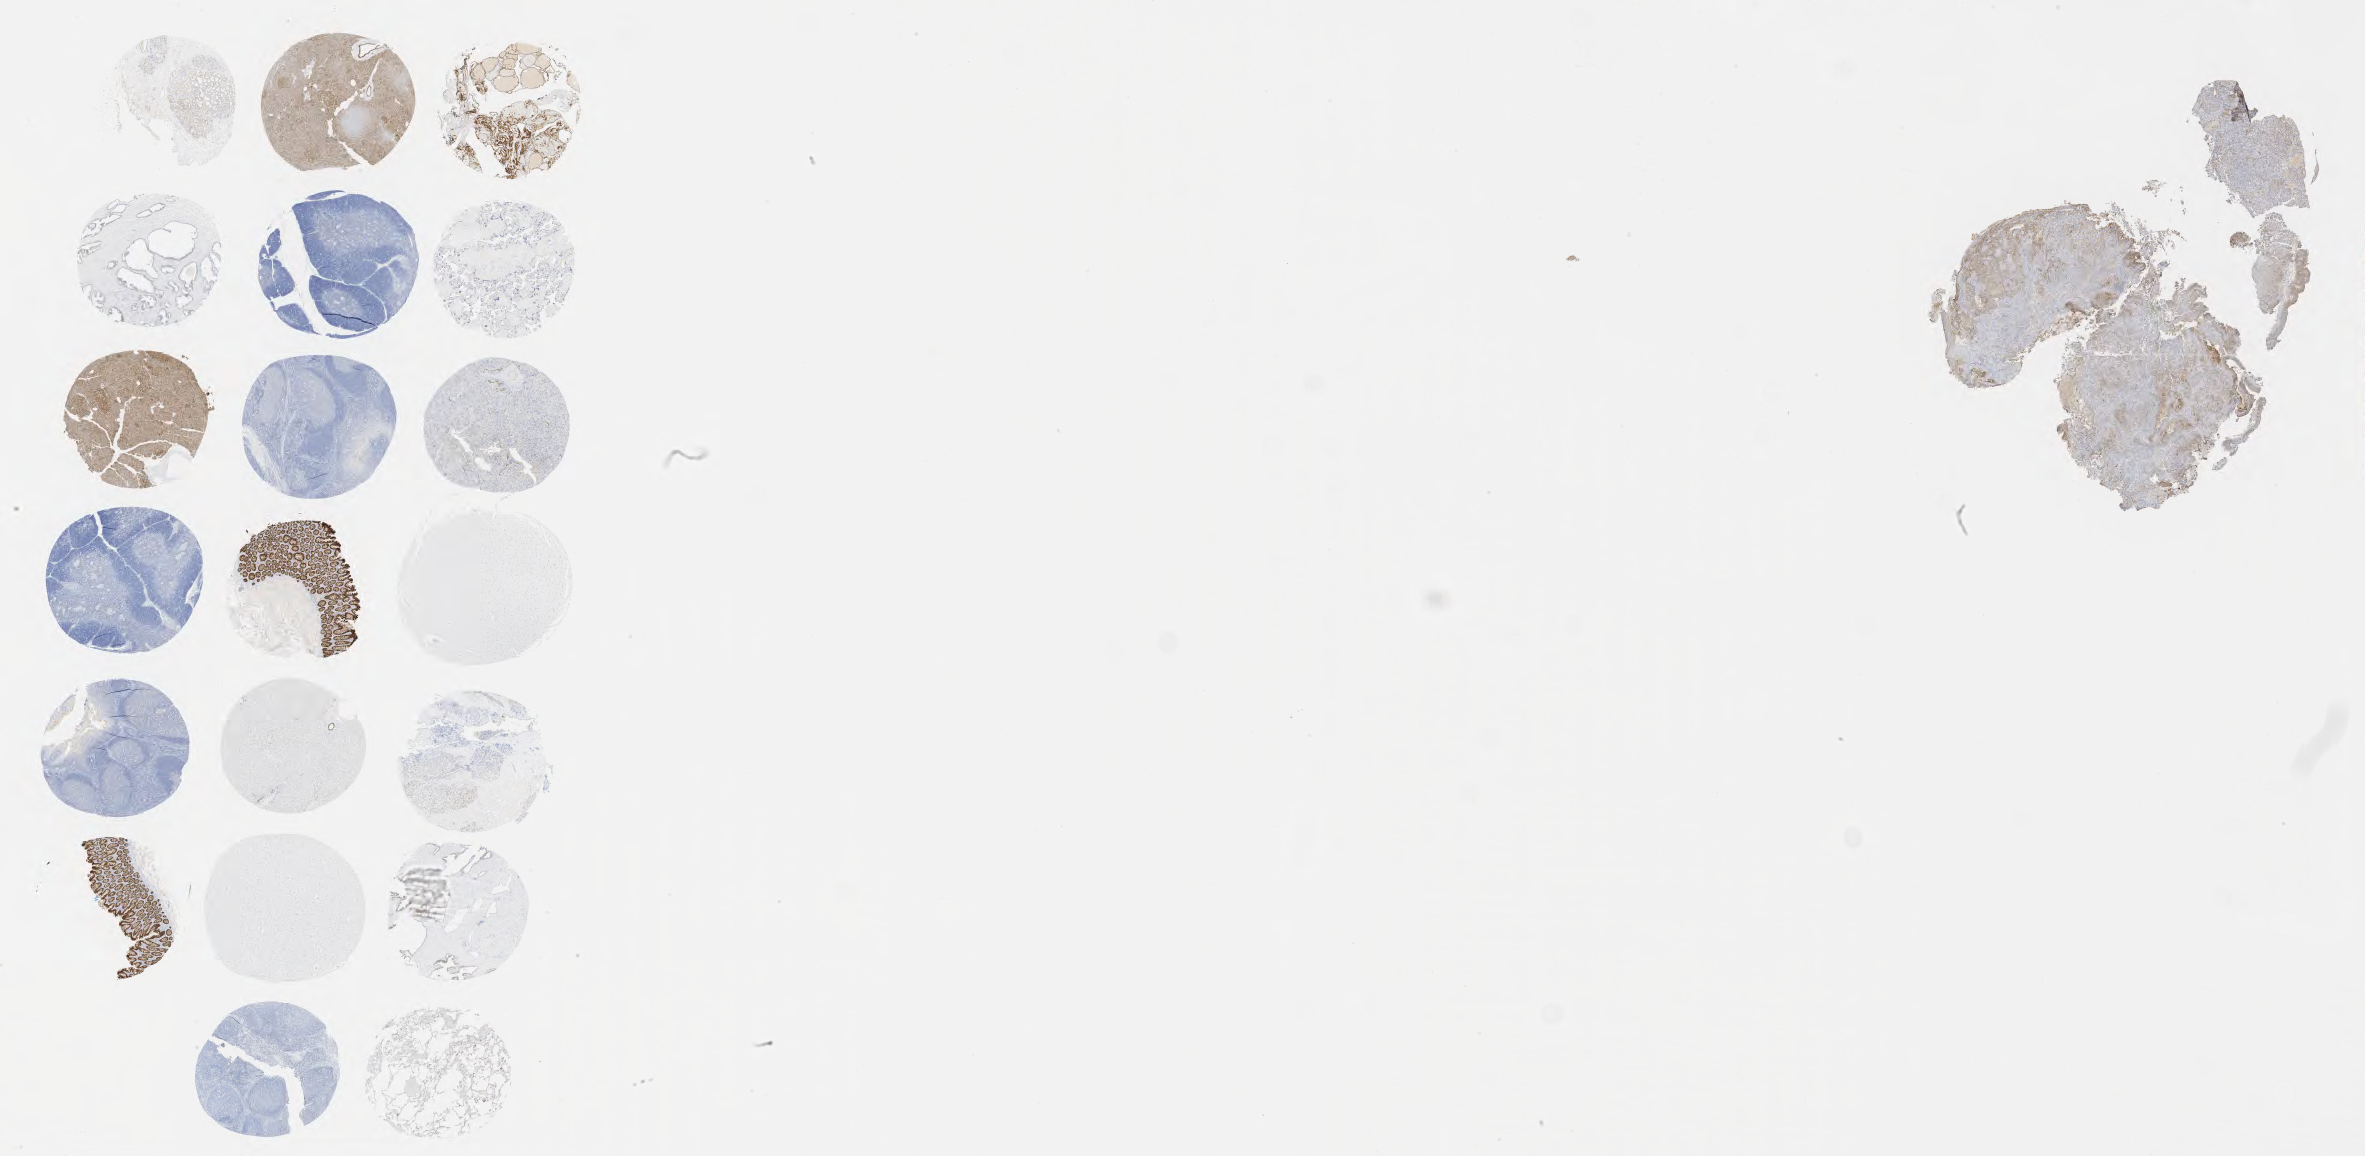
IHC for Ber-EP4, whole-slide image — shown as a low-resolution overview of the whole scanned area (about 38.2 x 18.7 mm), specimen: tumor tissue, anatomic site: cervix. Patient female; aged 56.
Histologic diagnosis: Adenocarcinoma, NOS.